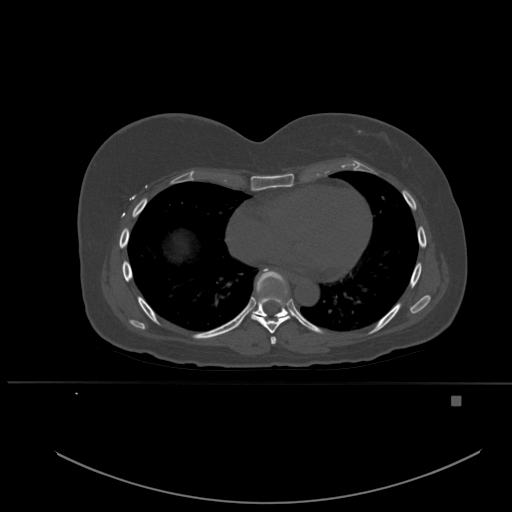
CT including the spine, one axial slice. Bone window (W 1800 / L 400 HU). 1.5 mm slice thickness. 512 × 512 image matrix, field of view 443 × 443 mm. Patient: female, 49 years. Case-level facts recorded for this patient, not image findings: primary cancer: breast; vertebrae with lytic lesions (as recorded): L3, T12, L4.
Structures marked on this image (semi-automatically segmented with operator editing):
- T6 vertebra: bounding box (x1, y1, x2, y2) in pixels: (270, 336, 277, 344)
- T7 vertebra: (251, 289, 290, 334)
- T8 vertebra: (252, 268, 292, 317)